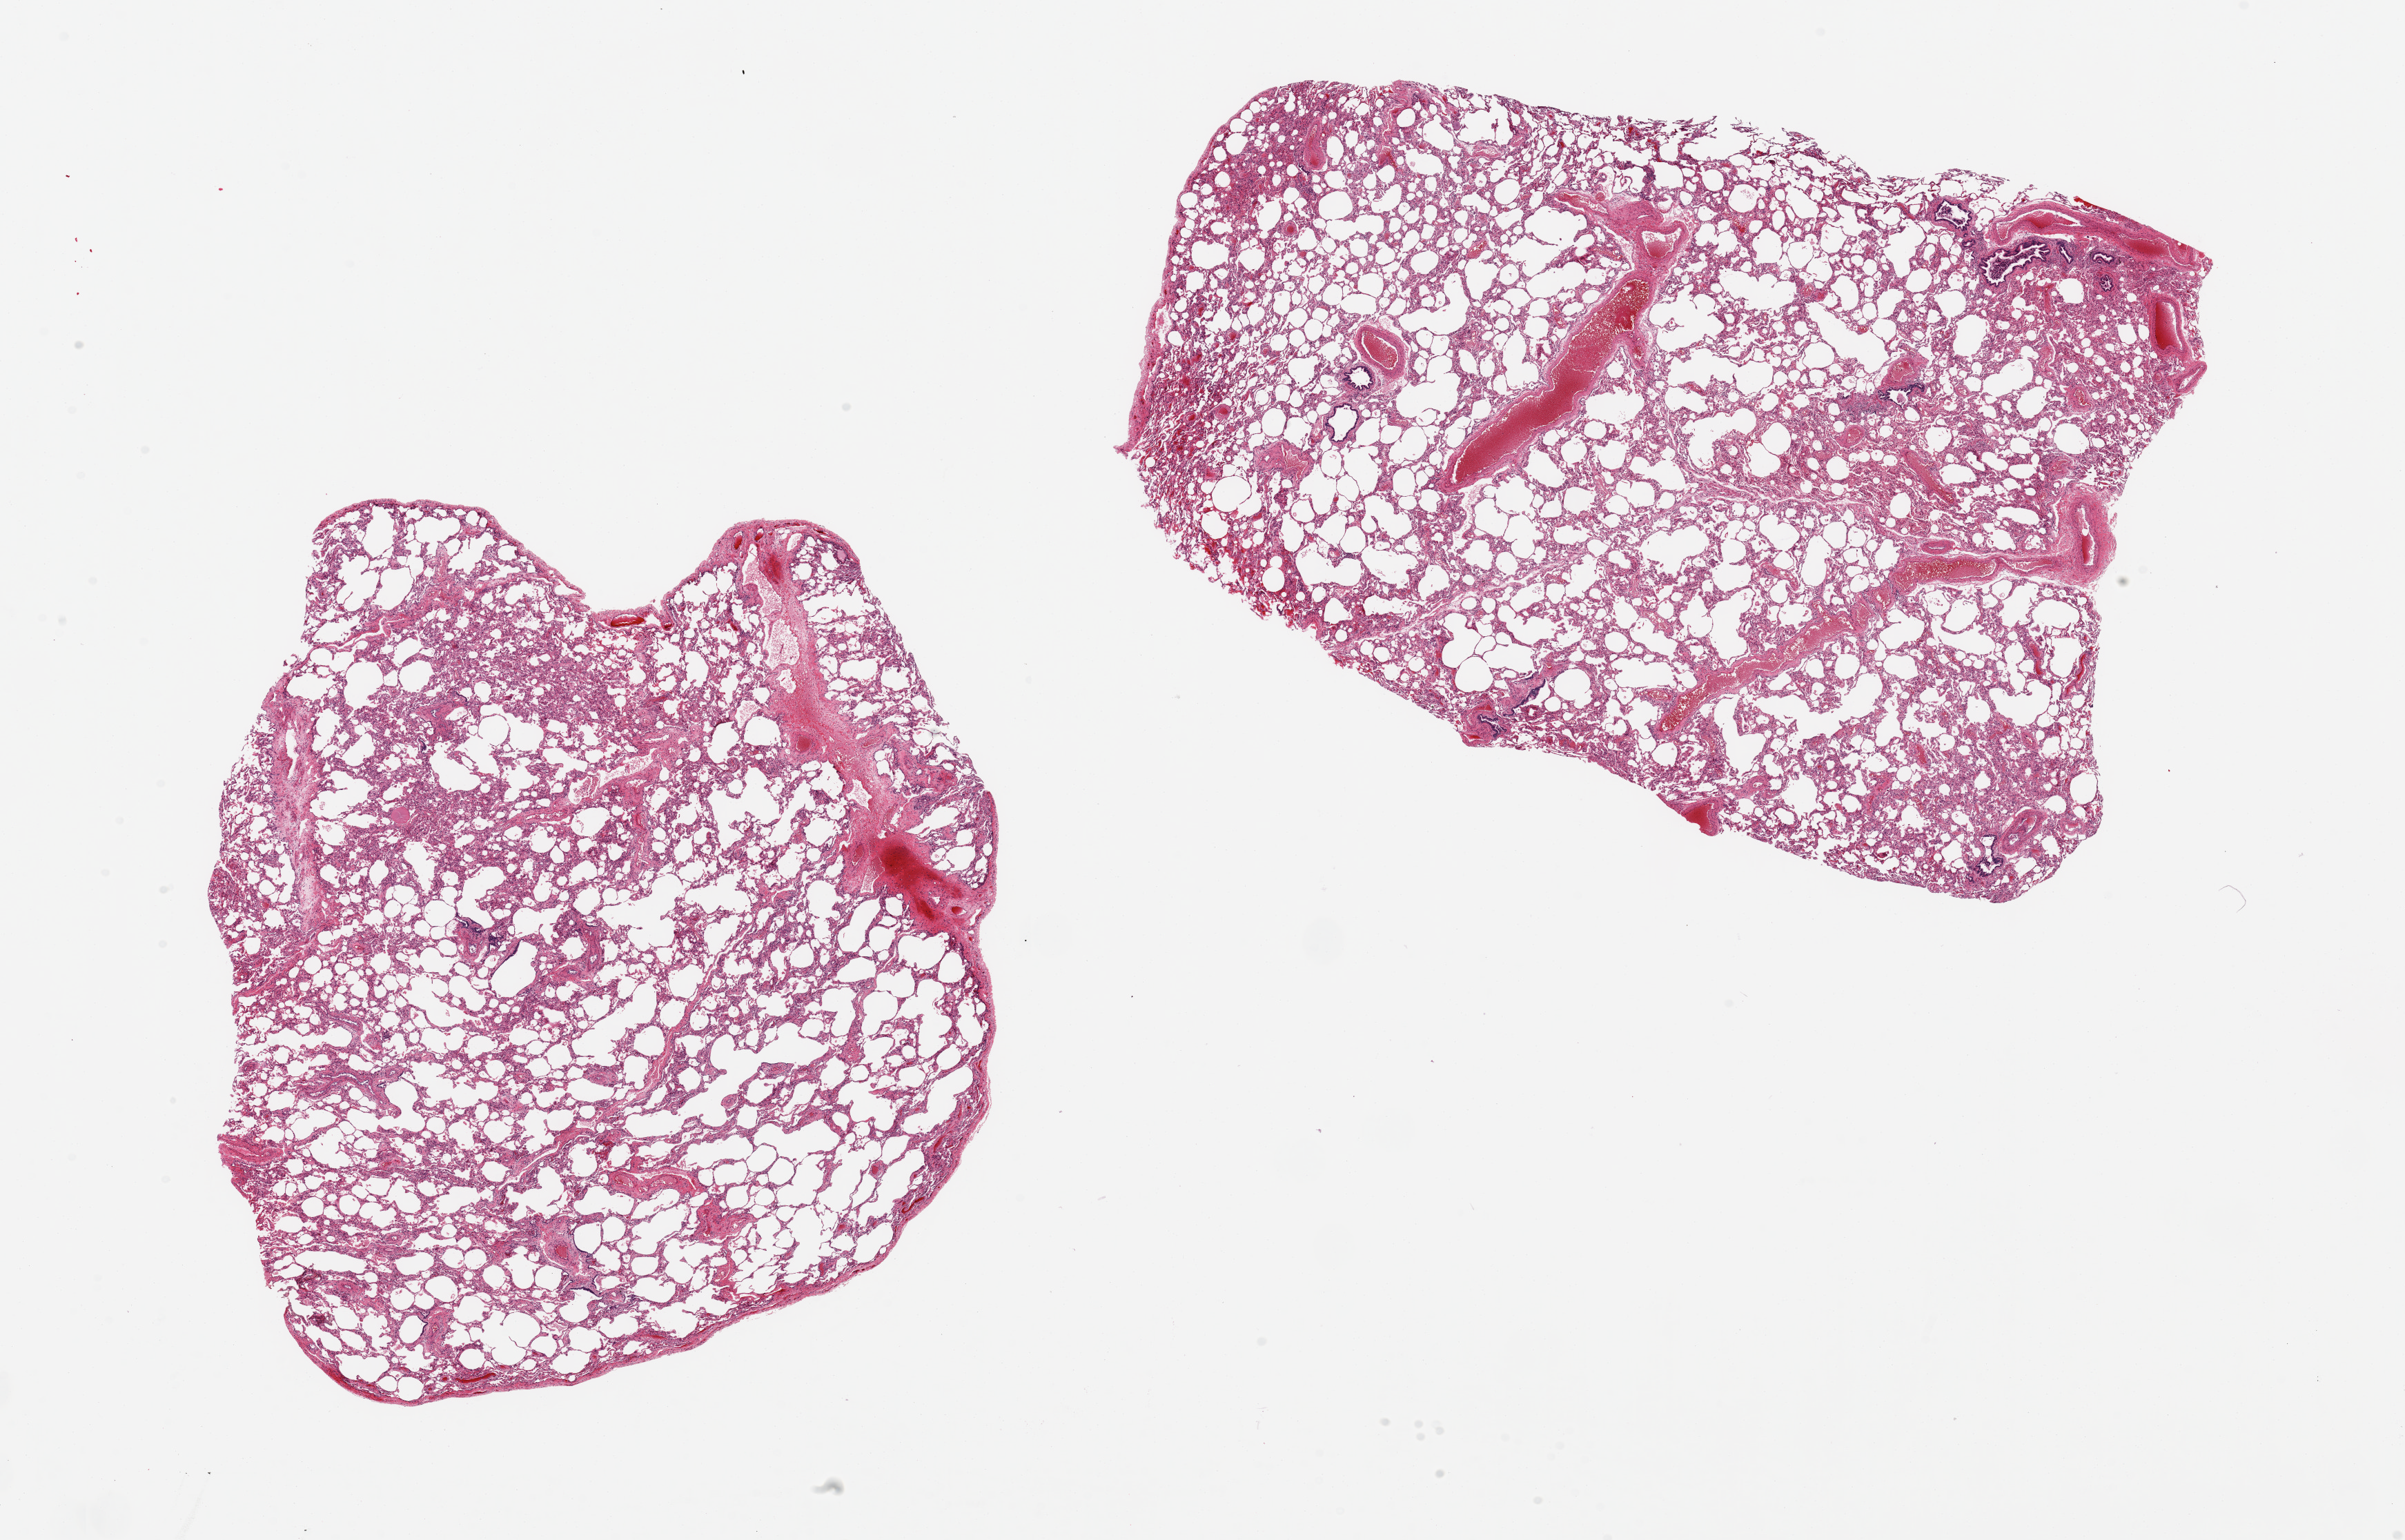
Hematoxylin and eosin (H&E) whole-slide image — low-resolution overview of the scanned area, about 27.6 x 17.7 mm, PAXgene-fixed paraffin-embedded (PFPE) section, sampled site (target tissue): lung, tissue donor sample. Male donor.
Pathologist's review note for this sample: 2 pieces 11x8 & 10x8 mm; no congestion or exudates.